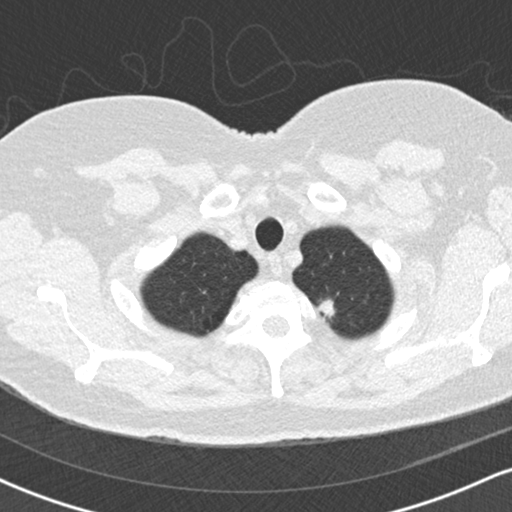
Low-dose screening chest CT, one axial slice; slice 151 of 170 in the series (ordered by position); reconstruction kernel B30f; lung window (W 1500 / L -600 HU); 512 × 512 image matrix.
Outlined on this slice (expert manual segmentation):
- lesion 1 (tumor, upper lobe of left lung): bounding box <317,300,334,317> (left, top, right, bottom; pixels)